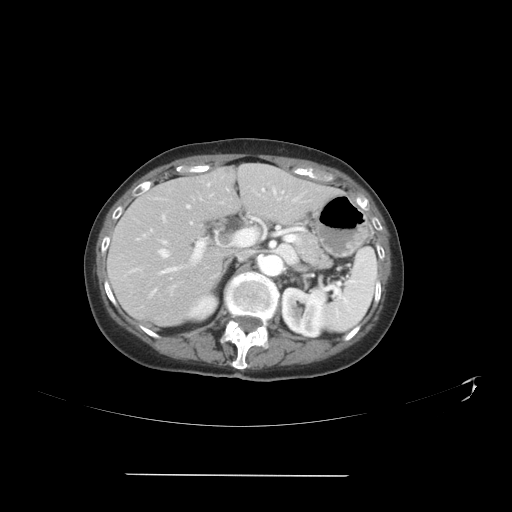
Contrast-enhanced abdominal CT, one axial slice; position 23 of 41 along the scan axis; 120 kVp; intravenous contrast given; soft-tissue window (W 400 / L 40 HU); 5 mm slice thickness; 512 × 512 image matrix. Female patient, age 74 years. Case-level facts recorded for this patient, not image findings: diagnosis: colorectal cancer liver metastases, imaged before liver resection; multiple liver metastases: yes; largest metastasis: 3.3 cm.
Outlined on this slice (outlined manually by an expert reader):
- hepatic veins: box from (x=151, y=194) to (x=280, y=295) px
- liver: (x=109, y=164)–(x=336, y=325)
- planned liver remnant (the part of the liver to remain after resection): (x=117, y=165)–(x=317, y=245)
- portal vein (with intrahepatic branches): (x=151, y=189)–(x=284, y=273)